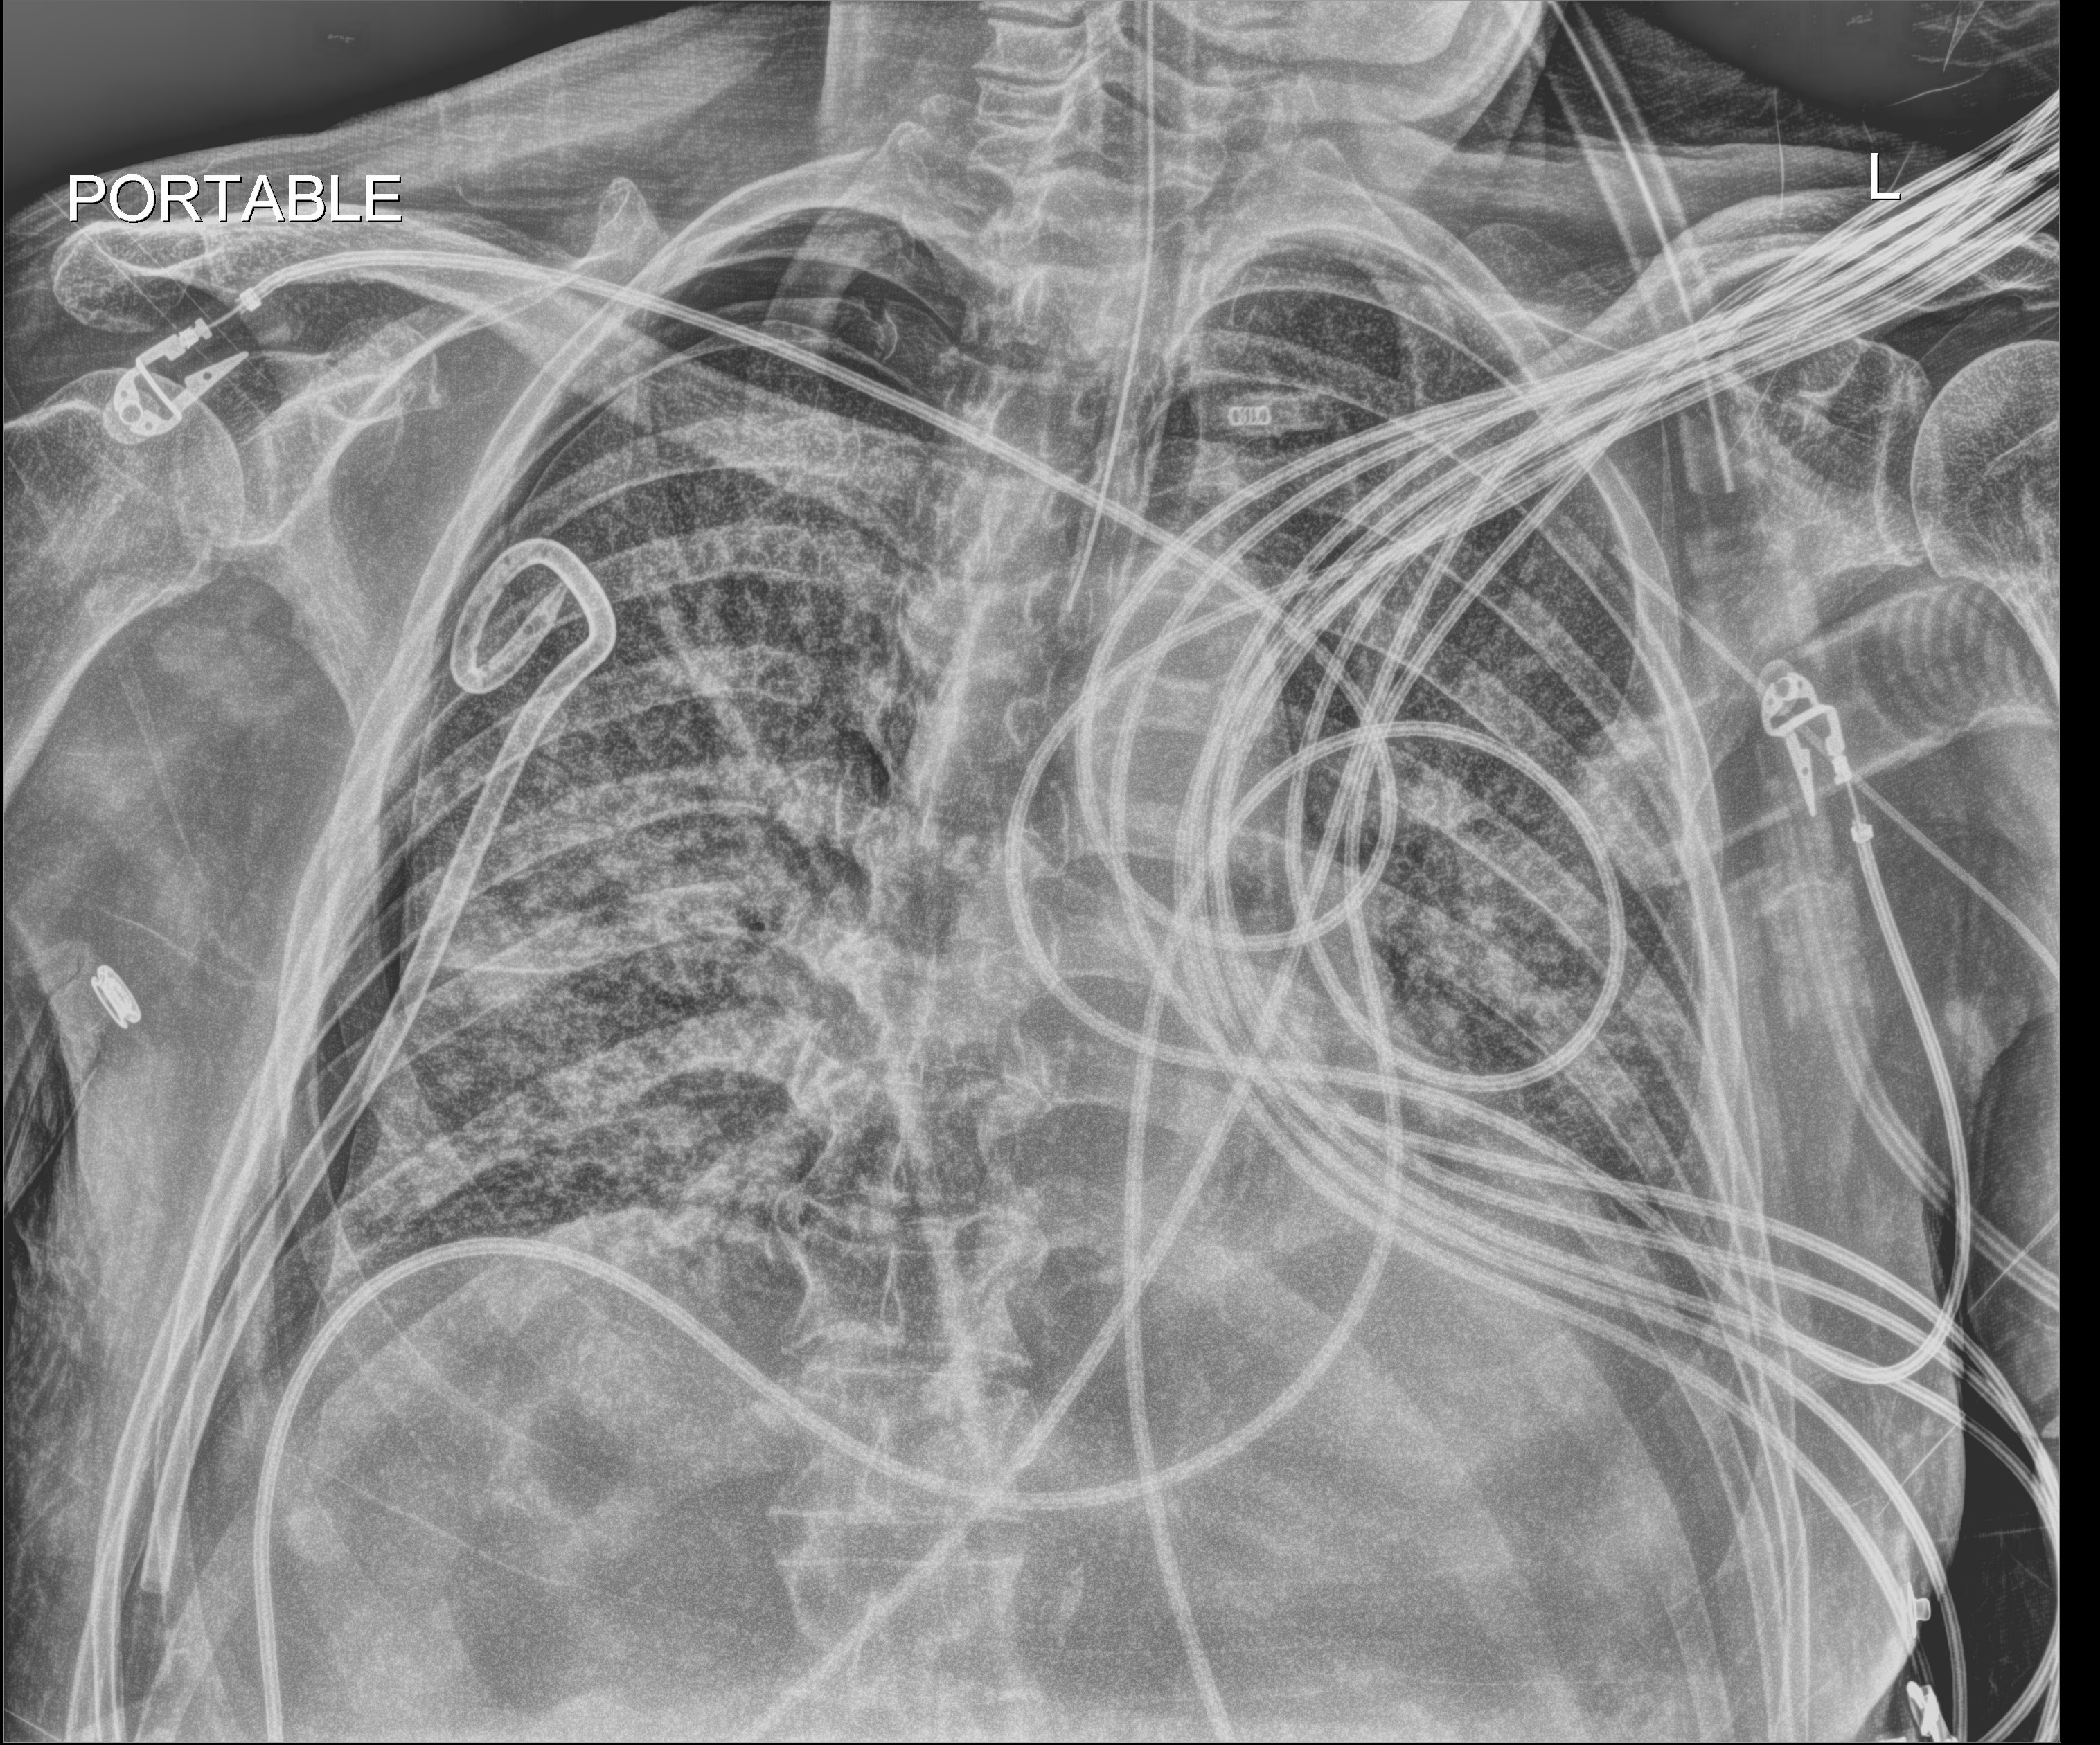
Chest X-ray (portable); anteroposterior (AP) projection. Male patient hospitalised with COVID-19, age 75–90 years.
Hospital-stay facts (about this admission, not read from this image; timing relative to this image not recorded): chronic kidney disease (admission record): no; admitted to intensive care during this hospital stay: yes; mechanically ventilated during this hospital stay: yes.